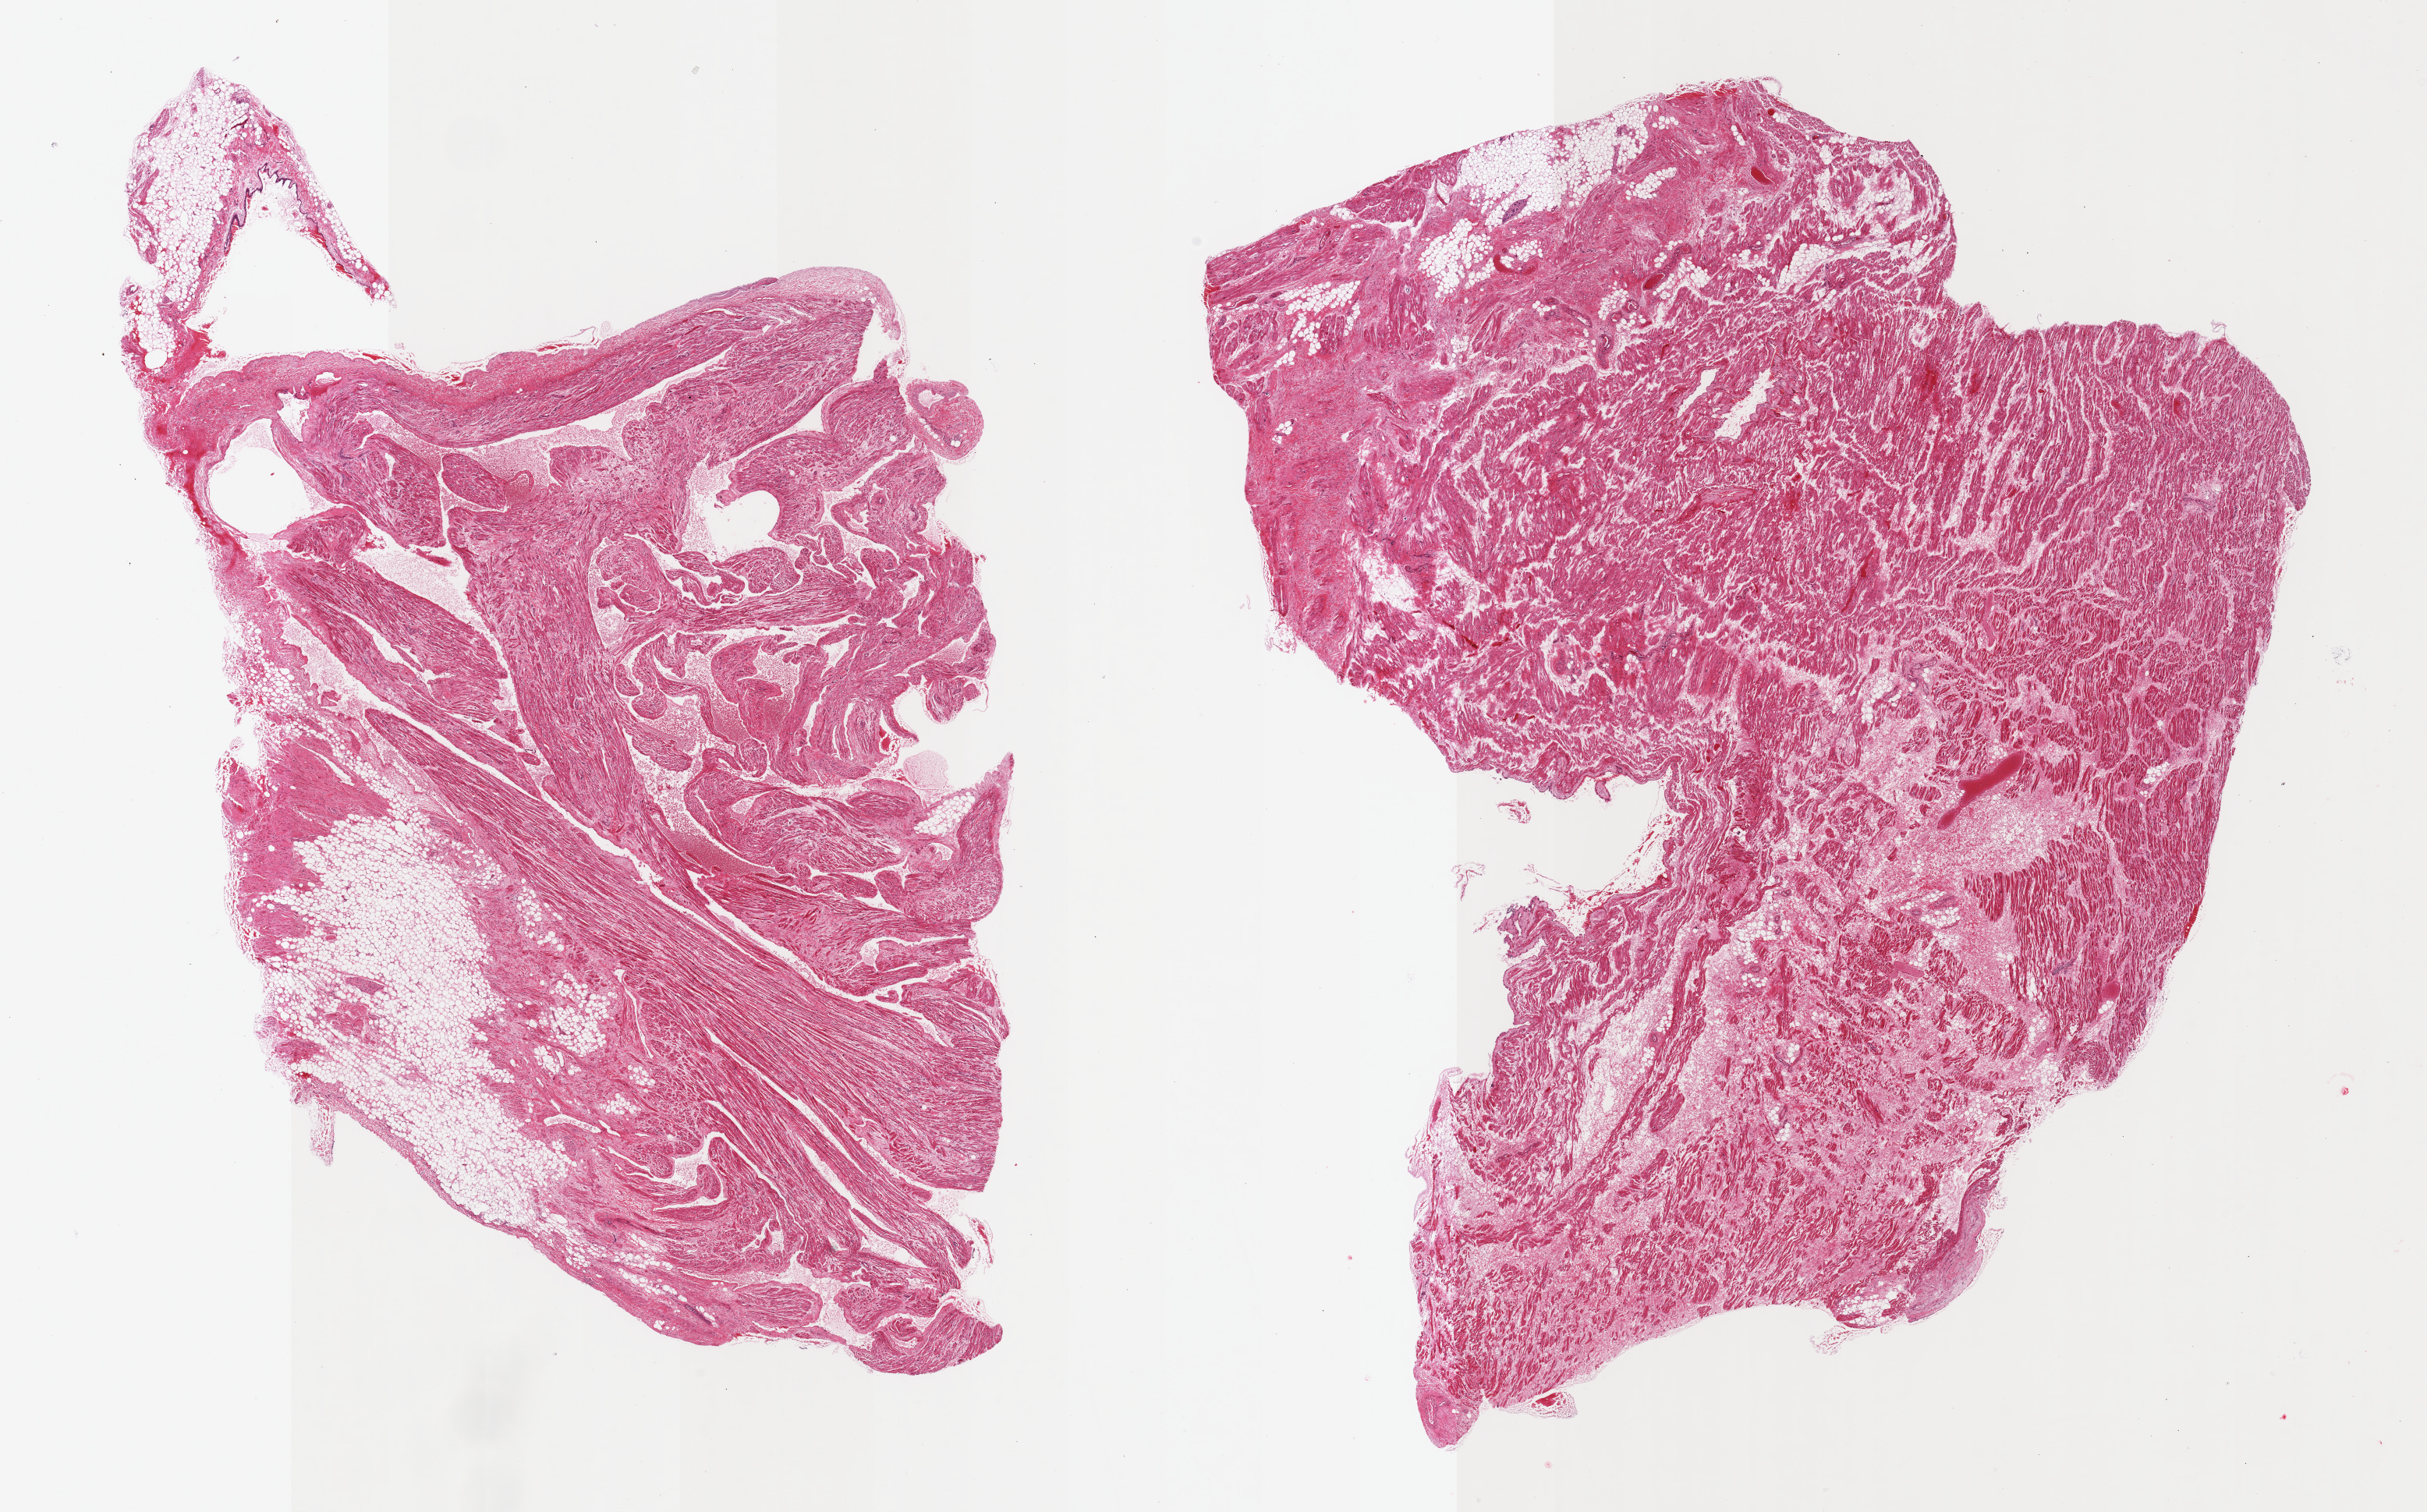
Whole-slide image, haematoxylin and eosin stain — a low-resolution overview of the entire scanned area, about 24.6 x 15.3 mm (from a 20x scan), PAXgene-fixed, paraffin-embedded tissue, sampled site (target tissue): auricular appendage, donor tissue sample.
Reviewer comment on this tissue sample: 2 pieces; 20-30% fibrous and fatty content.